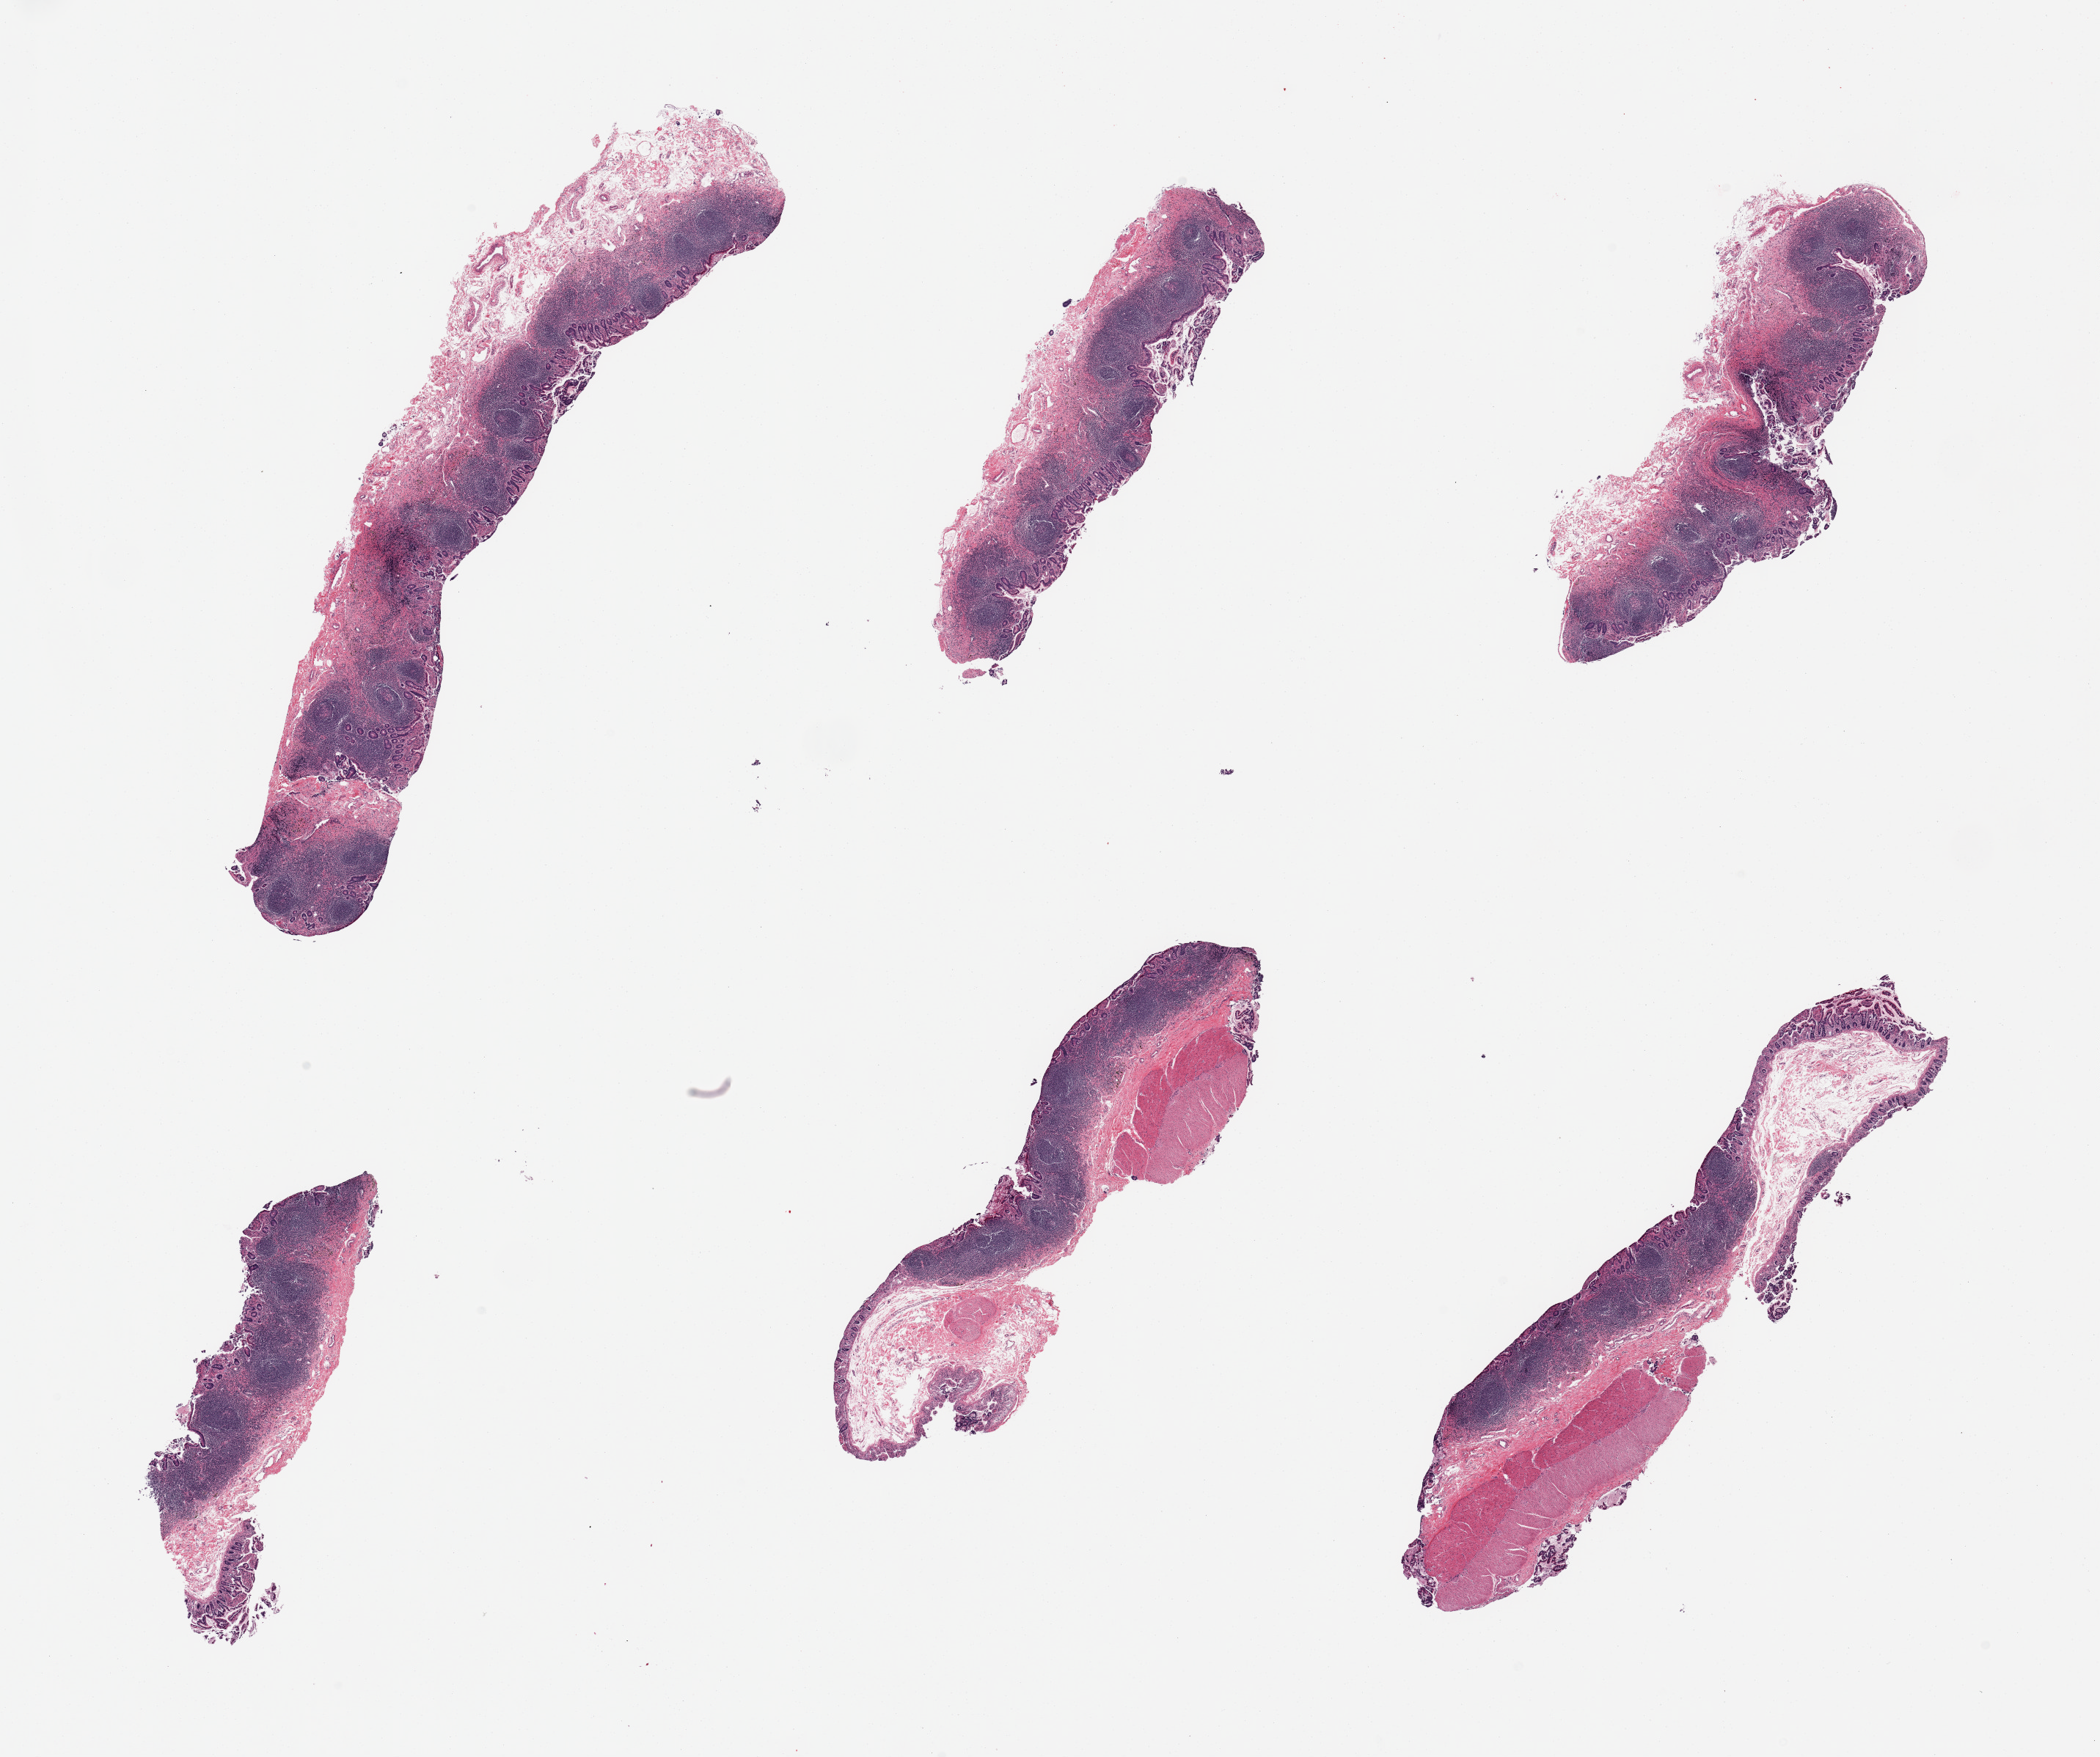
Haematoxylin and eosin whole-slide image — low-resolution overview of the scanned area, about 22.6 x 18.9 mm. PAXgene-fixed, paraffin-embedded tissue. Sampled site (target tissue): ileum. Donor tissue sample. Donor: female.
Reviewer comment on this tissue sample: 6 pieces, well preserved, target lymphoid aggregates are ~60% of tissue, excellent specimen.